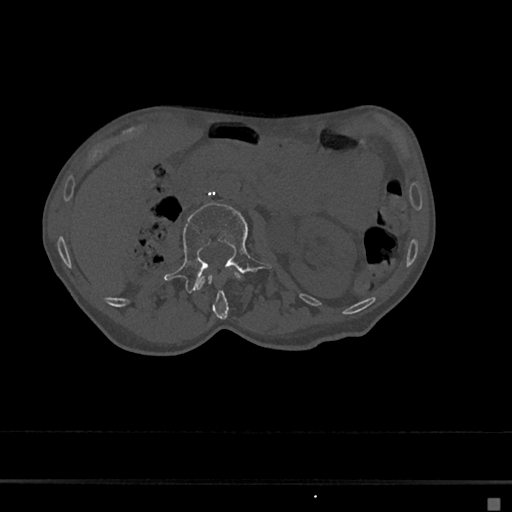
CT including the spine, one axial slice. 120 kVp. Bone window (W 1800 / L 400 HU). 0.5 mm slice thickness. 512 × 512 image matrix, field of view 360 × 360 mm. Female patient, age 68 years. Case-level facts recorded for this patient, not image findings: primary cancer: renal.
Outlined on this slice (semi-automatic segmentation, software-assisted and operator-edited):
- L1 vertebra: box from (x=197, y=271) to (x=242, y=319) px
- L2 vertebra: (x=164, y=203)–(x=273, y=293)